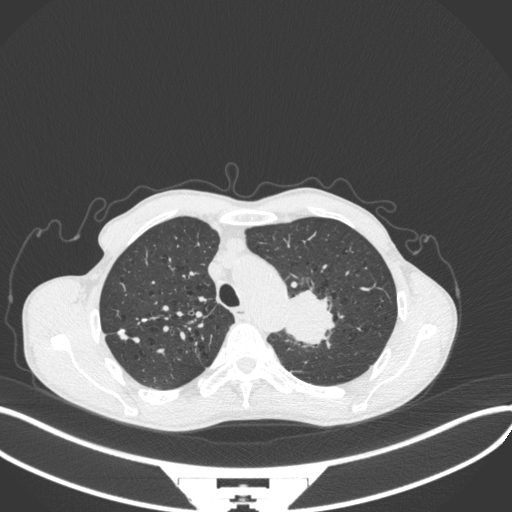
Chest CT, one axial slice. Slice 324 of 394 in the series (ordered by position). Reconstruction kernel B31f. 120 kVp. Lung window (W 1500 / L -600 HU). 1 mm slice thickness. 512 × 512 image matrix, field of view 400 × 400 mm. Patient: male, 65 years. From the clinical record (not read from this slice): clinical TNM (as recorded): T2b N0 M0.
Structures marked on this image (rectangle marked by the reading radiologist):
- lung tumour (recorded histology: adenocarcinoma): box from (x=283, y=284) to (x=340, y=352) px